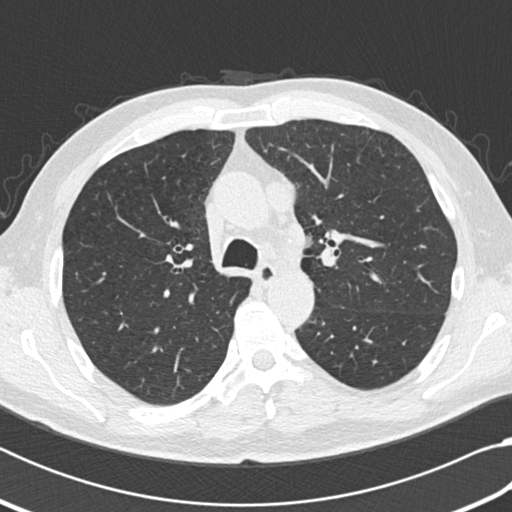
Axial slice from a low-dose chest CT screening exam. Third screening round (two years after baseline). Lung window (W 1500 / L -600 HU). 2 mm slice thickness. Standard (soft-tissue) reconstruction kernel (B30f). Slice 65 of 207 in the series. Male, age 64 years at enrolment. Current smoker at enrolment.
Expert reader's lesion annotation, box from (x=252, y=177) to (x=291, y=215) px. No non-calcified nodule or mass ≥4 mm was recorded by the screening reader at this exam. Official screen result: negative screen, significant abnormalities not suspicious for lung cancer. Participant outcome: lung cancer diagnosed 163 days after this screen — small cell carcinoma, NOS, mediastinum, stage IV (AJCC 6th edition).